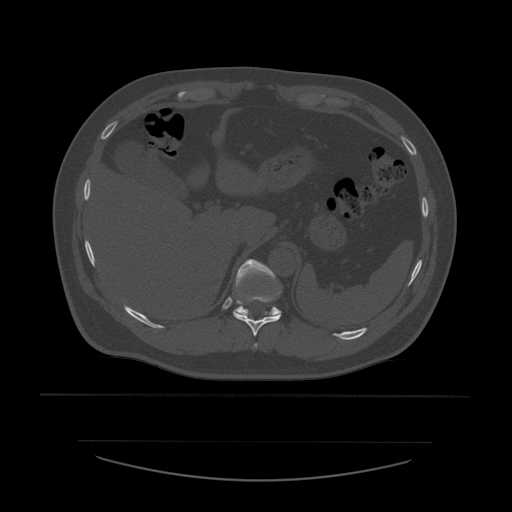
CT including the spine, one axial slice. Position 289 of 532 along the scan axis. Reconstruction kernel STANDARD. Bone window (W 1800 / L 400 HU). 1.25 mm slice thickness. 512 × 512 image matrix, field of view 441 × 441 mm. Patient age 44 years. Case-level facts recorded for this patient, not image findings: primary cancer: soft tissue sarcoma.
Structures marked on this image (semi-automatic segmentation, software-assisted and operator-edited):
- T10 vertebra: box from (x=234, y=292) to (x=281, y=337) px
- T11 vertebra: (x=233, y=259)–(x=282, y=317)
- T9 vertebra: (x=254, y=343)–(x=258, y=348)